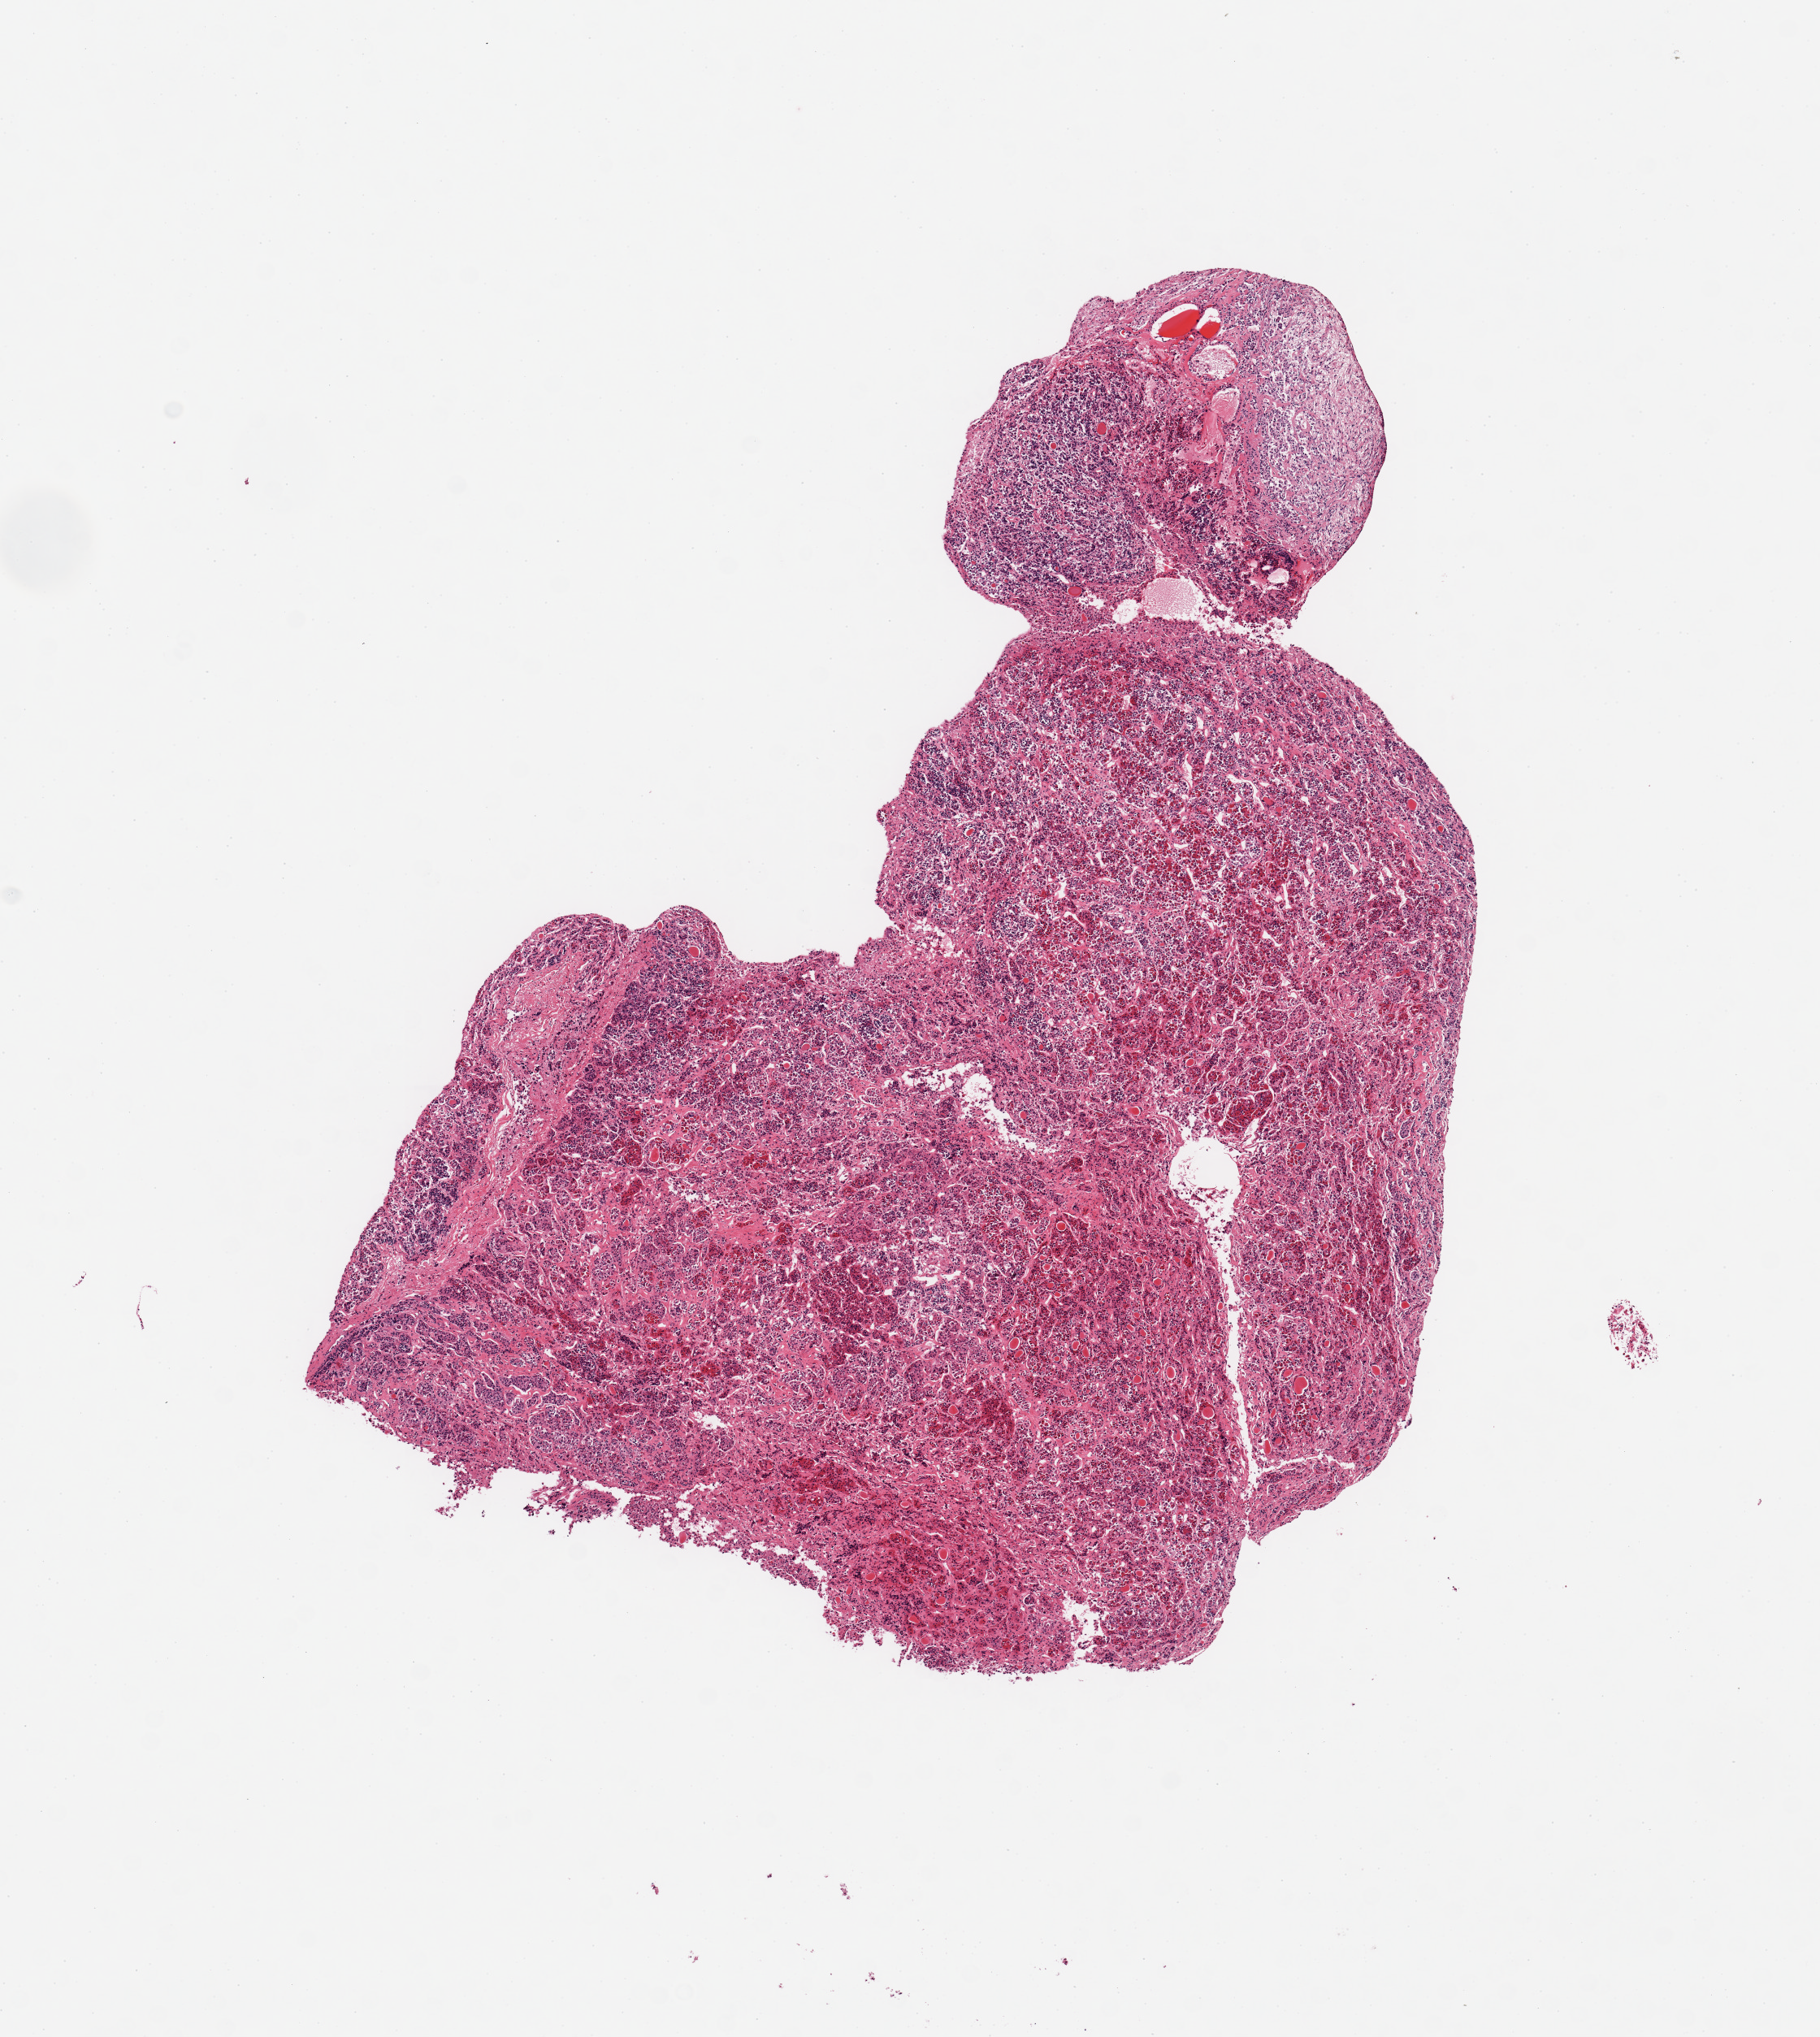
Whole-slide image, haematoxylin and eosin stain, shown as a low-resolution overview of the whole scanned area (about 8.9 x 9.9 mm); PAXgene-fixed paraffin-embedded (PFPE) section; target tissue: pituitary; tissue donor sample.
Review note (as recorded): 1 pieces; posterior lobe comprises <10%.